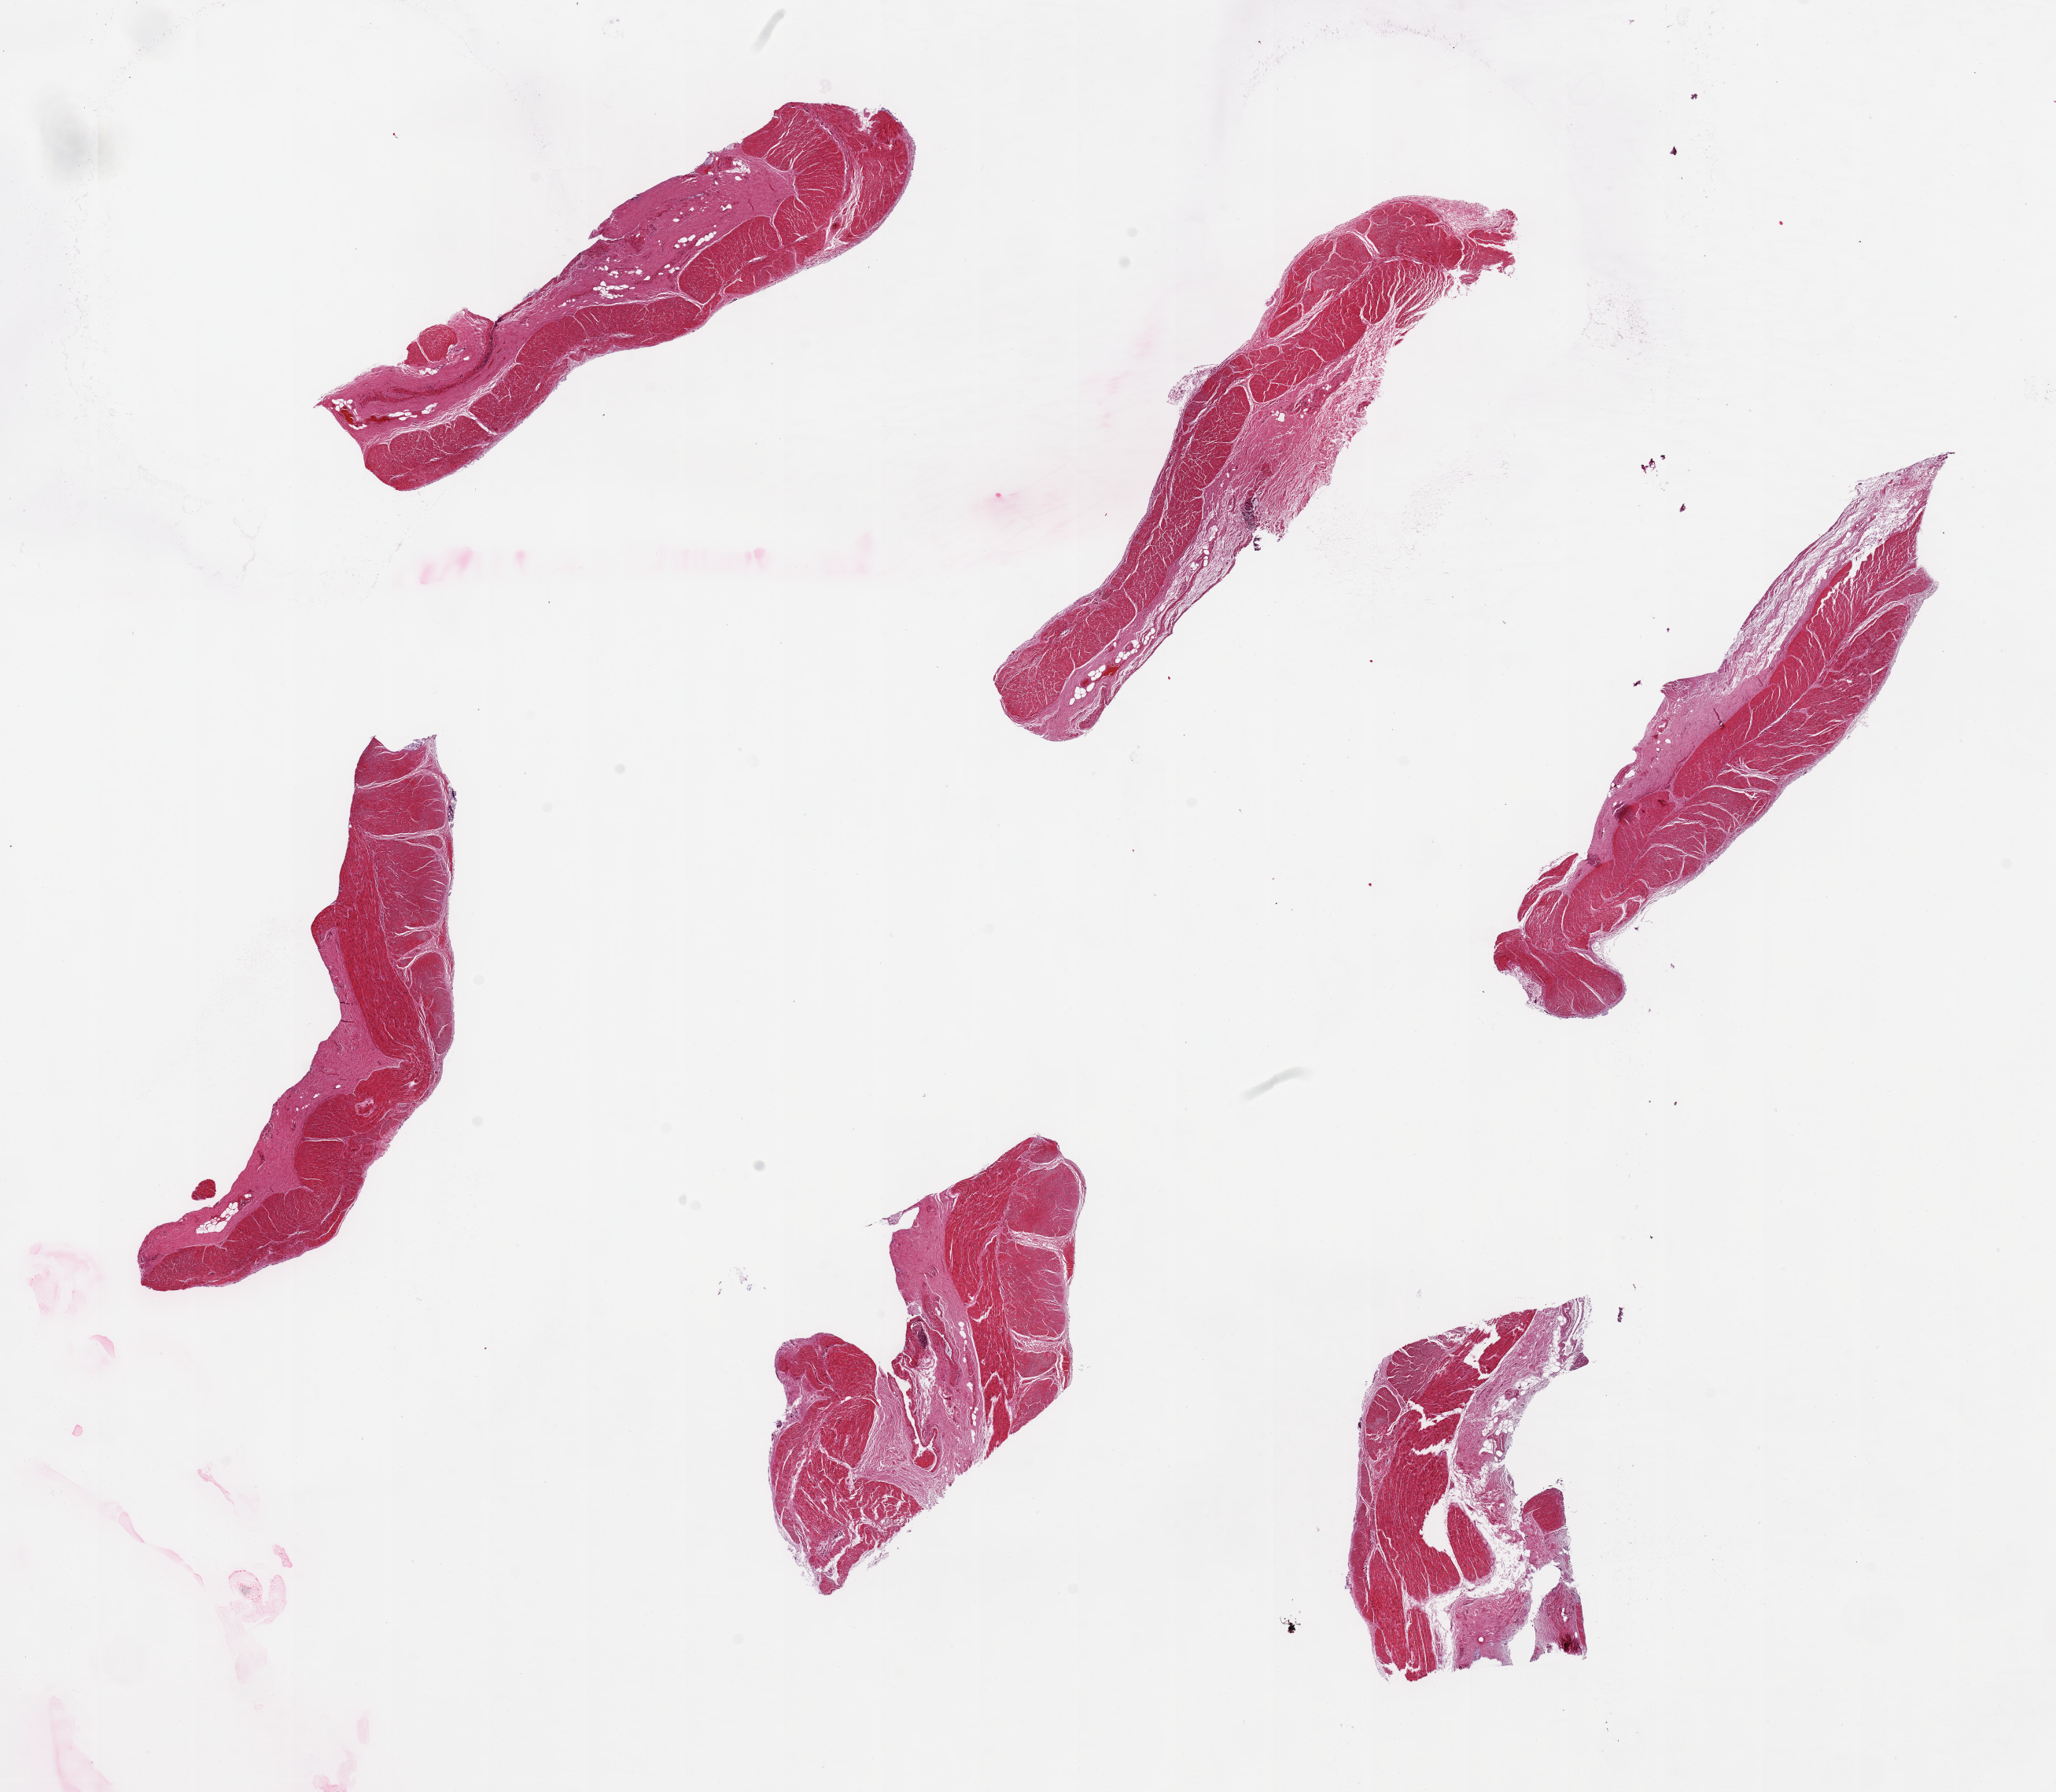
Whole-slide image, H&E stain, brightfield, low-resolution overview of the scanned area, about 20.7 x 18.0 mm (slide scanned at 20x). PAXgene-fixed, paraffin-embedded tissue. Sampled site (target tissue): sigmoid colon. Tissue donor sample.
Review note (as recorded): 6 pieces, up to 7x2mm; ~50% target muscularis present, rest is fat/stroma, rep target tissue.